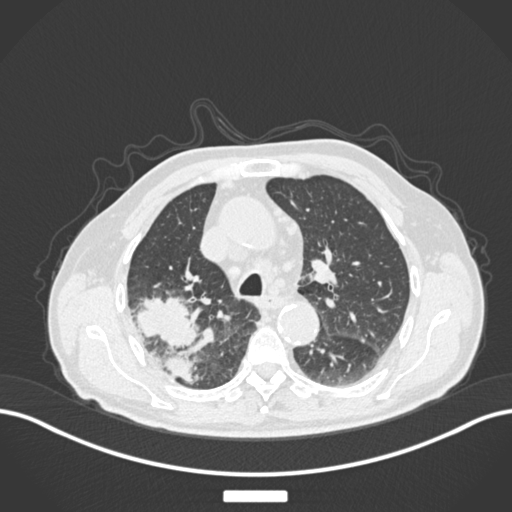
Chest CT, one axial slice; position 127 of 201 along the scan axis; reconstruction kernel B30f; lung window (W 1500 / L -600 HU); 1 mm slice thickness; 512 × 512 image matrix. Patient: male, 72 years. Case-level facts recorded for this patient, not image findings: clinical TNM (as recorded): T3 N2 M0.
Annotated regions visible in this slice (rectangle marked by the reading radiologist):
- lung tumour (recorded histology: adenocarcinoma): bounding box [x1, y1, x2, y2] px = [138, 292, 199, 389]